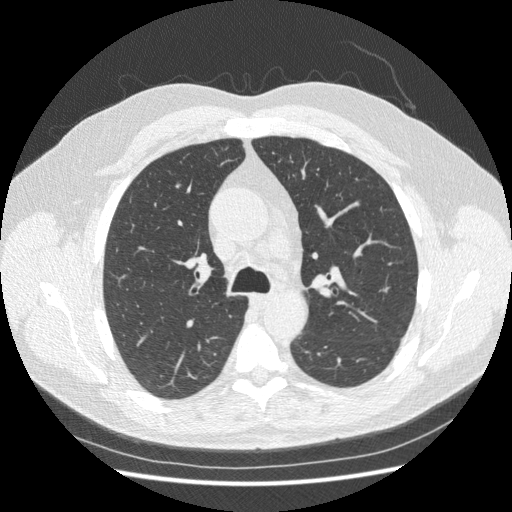
Low-dose screening chest CT, one axial slice; 120 kVp; lung window (W 1500 / L -600 HU); 1.25 mm slice thickness; 512 × 512 image matrix.
Annotated regions visible in this slice (expert manual segmentation):
- lesion 1 (tumor, upper lobe of right lung): bounding box [x1, y1, x2, y2] px = [174, 183, 181, 191]